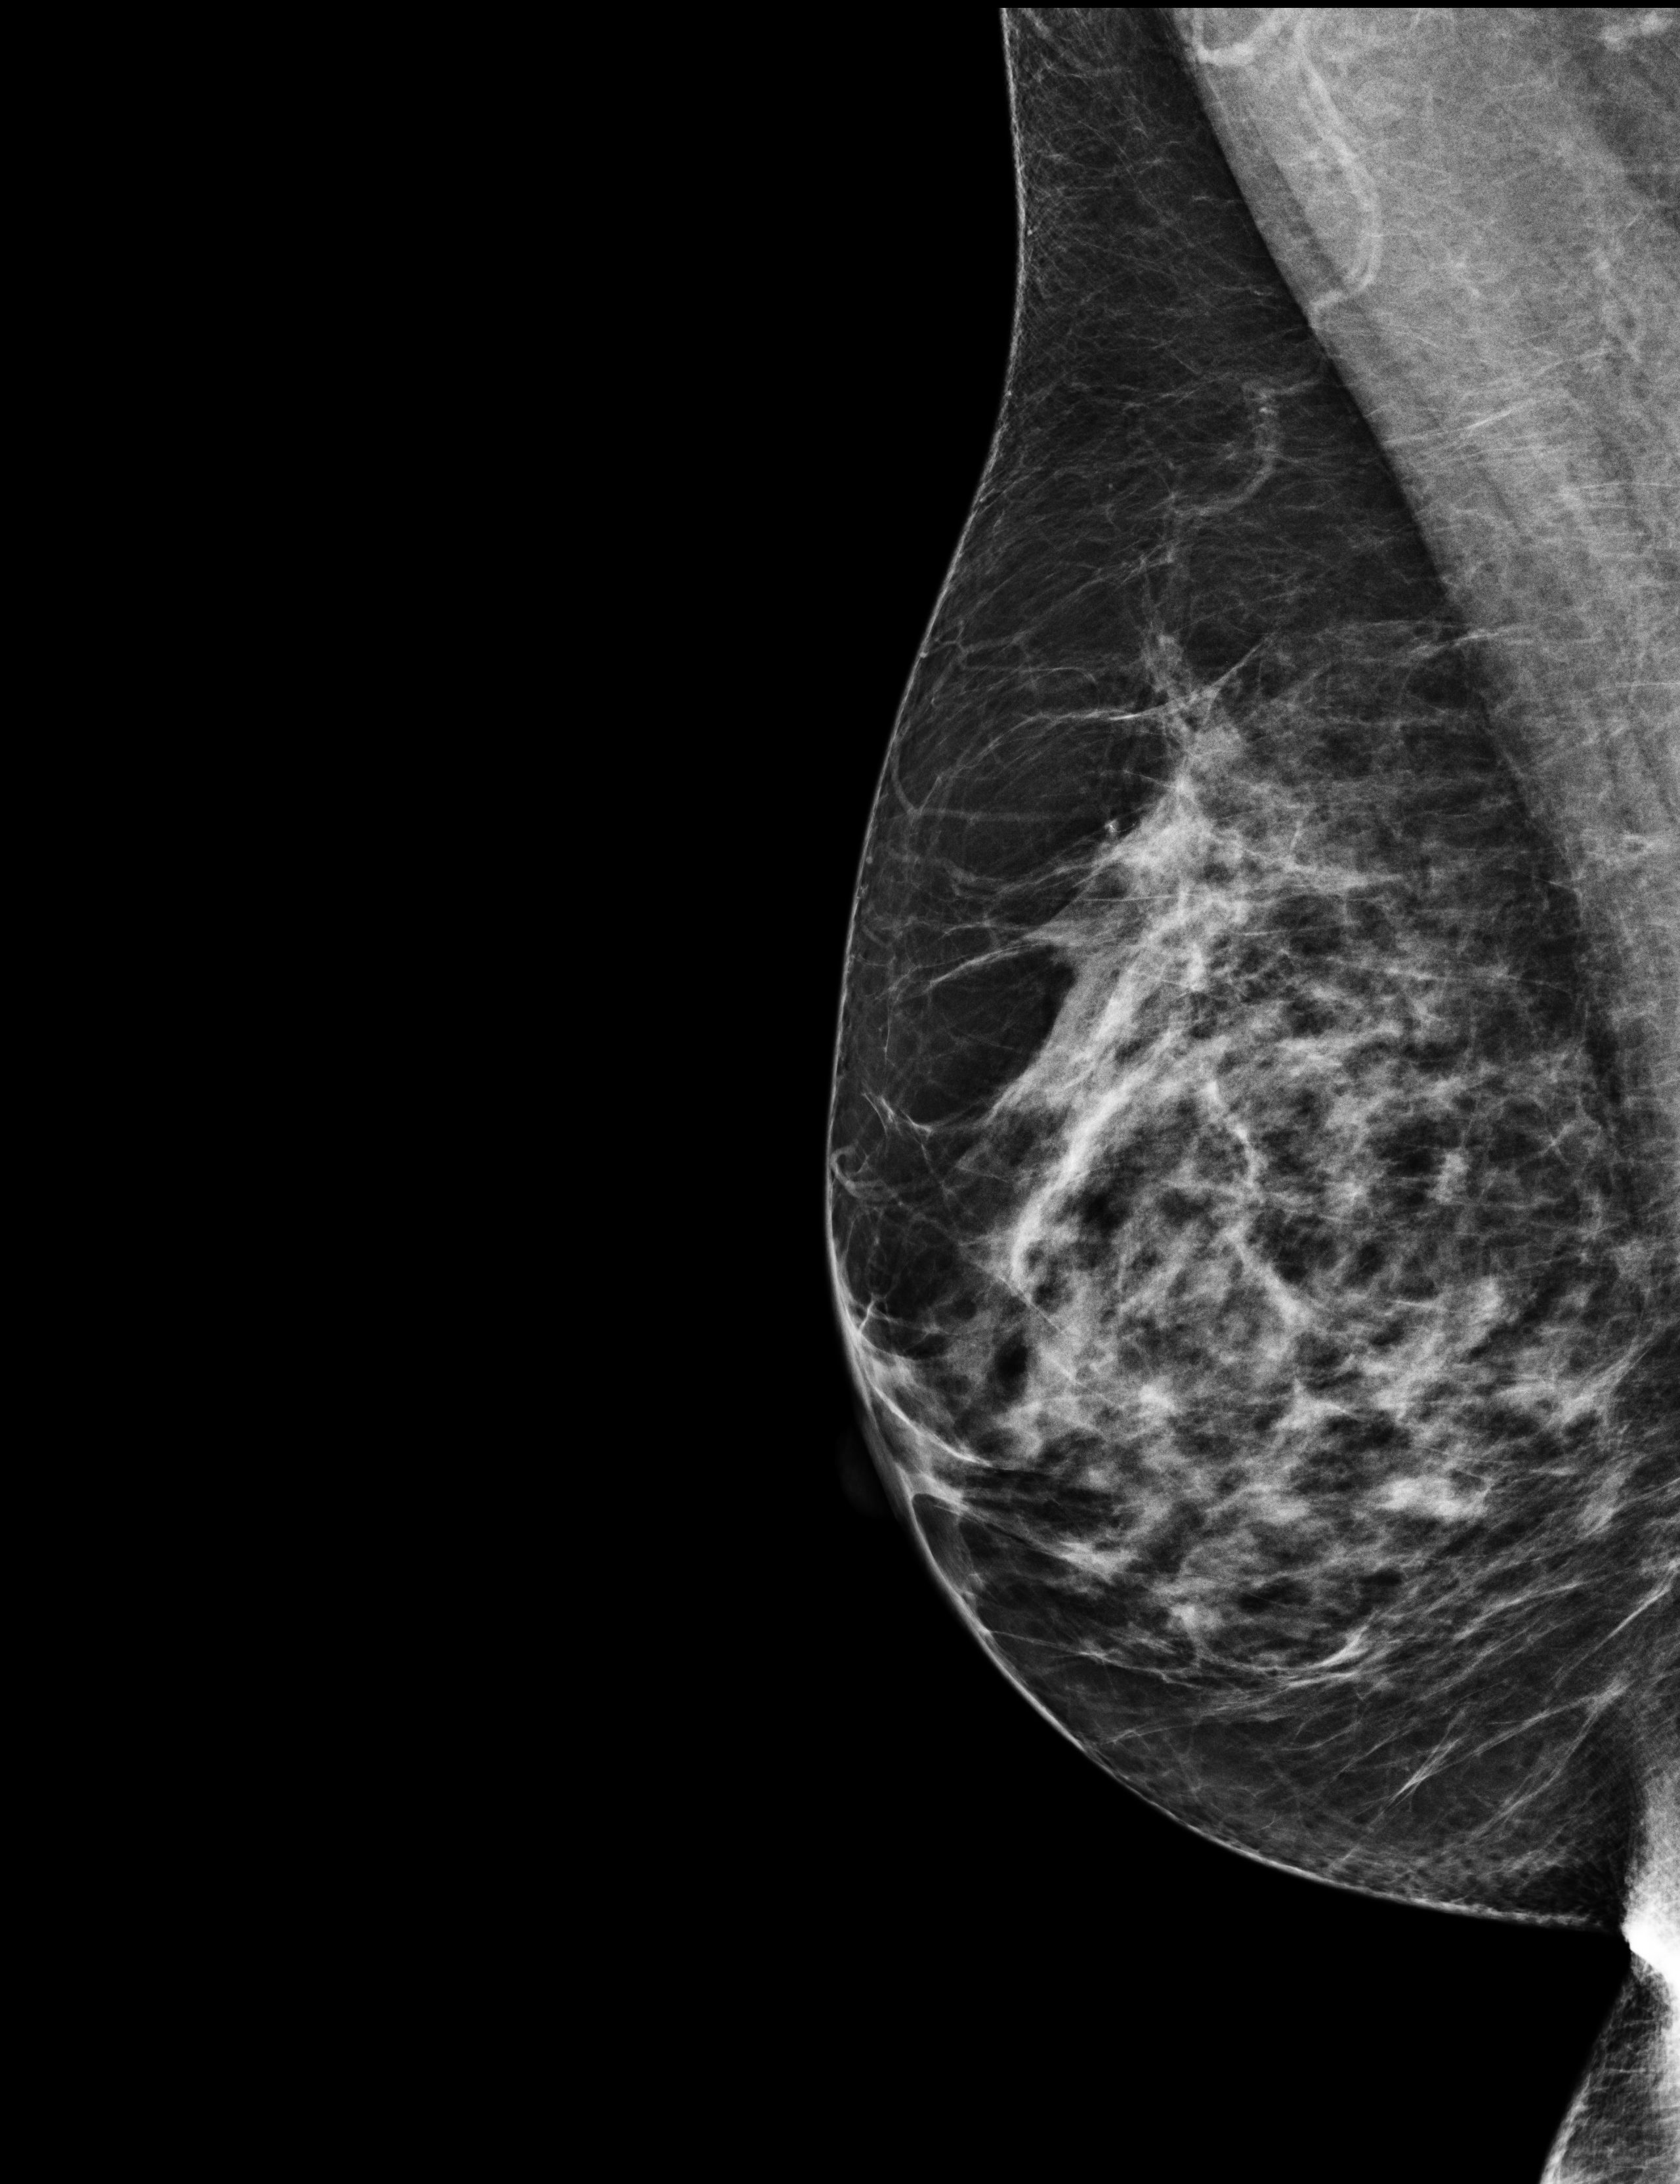
Screening examination, compressed breast thickness 57 mm. Patient: female, 59 years.
Image type: full-field digital mammogram. Breast: right. Projection: medio-lateral oblique projection.